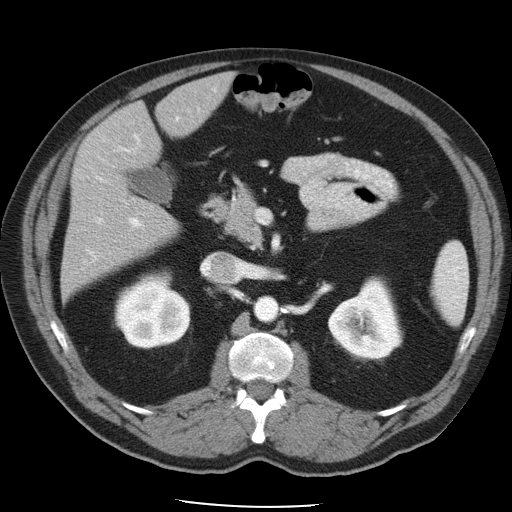
Contrast-enhanced abdominal CT, one axial slice. Position 25 of 49 along the scan axis. Intravenous contrast given. Soft-tissue window (W 400 / L 40 HU). 5 mm slice thickness. 512 × 512 image matrix, field of view 395 × 395 mm. Male patient, age 68 years. From the clinical record (not read from this slice): diagnosis: colorectal cancer liver metastases, imaged before liver resection; multiple liver metastases: yes; largest metastasis: 1.7 cm; disease in both lobes: no.
Structures marked on this image (manually delineated by an expert):
- hepatic veins: box from (x=97, y=219) to (x=246, y=280) px
- liver: (x=62, y=75)–(x=231, y=295)
- planned liver remnant (the part of the liver to remain after resection): (x=72, y=75)–(x=231, y=280)
- portal vein (with intrahepatic branches): (x=88, y=108)–(x=200, y=262)